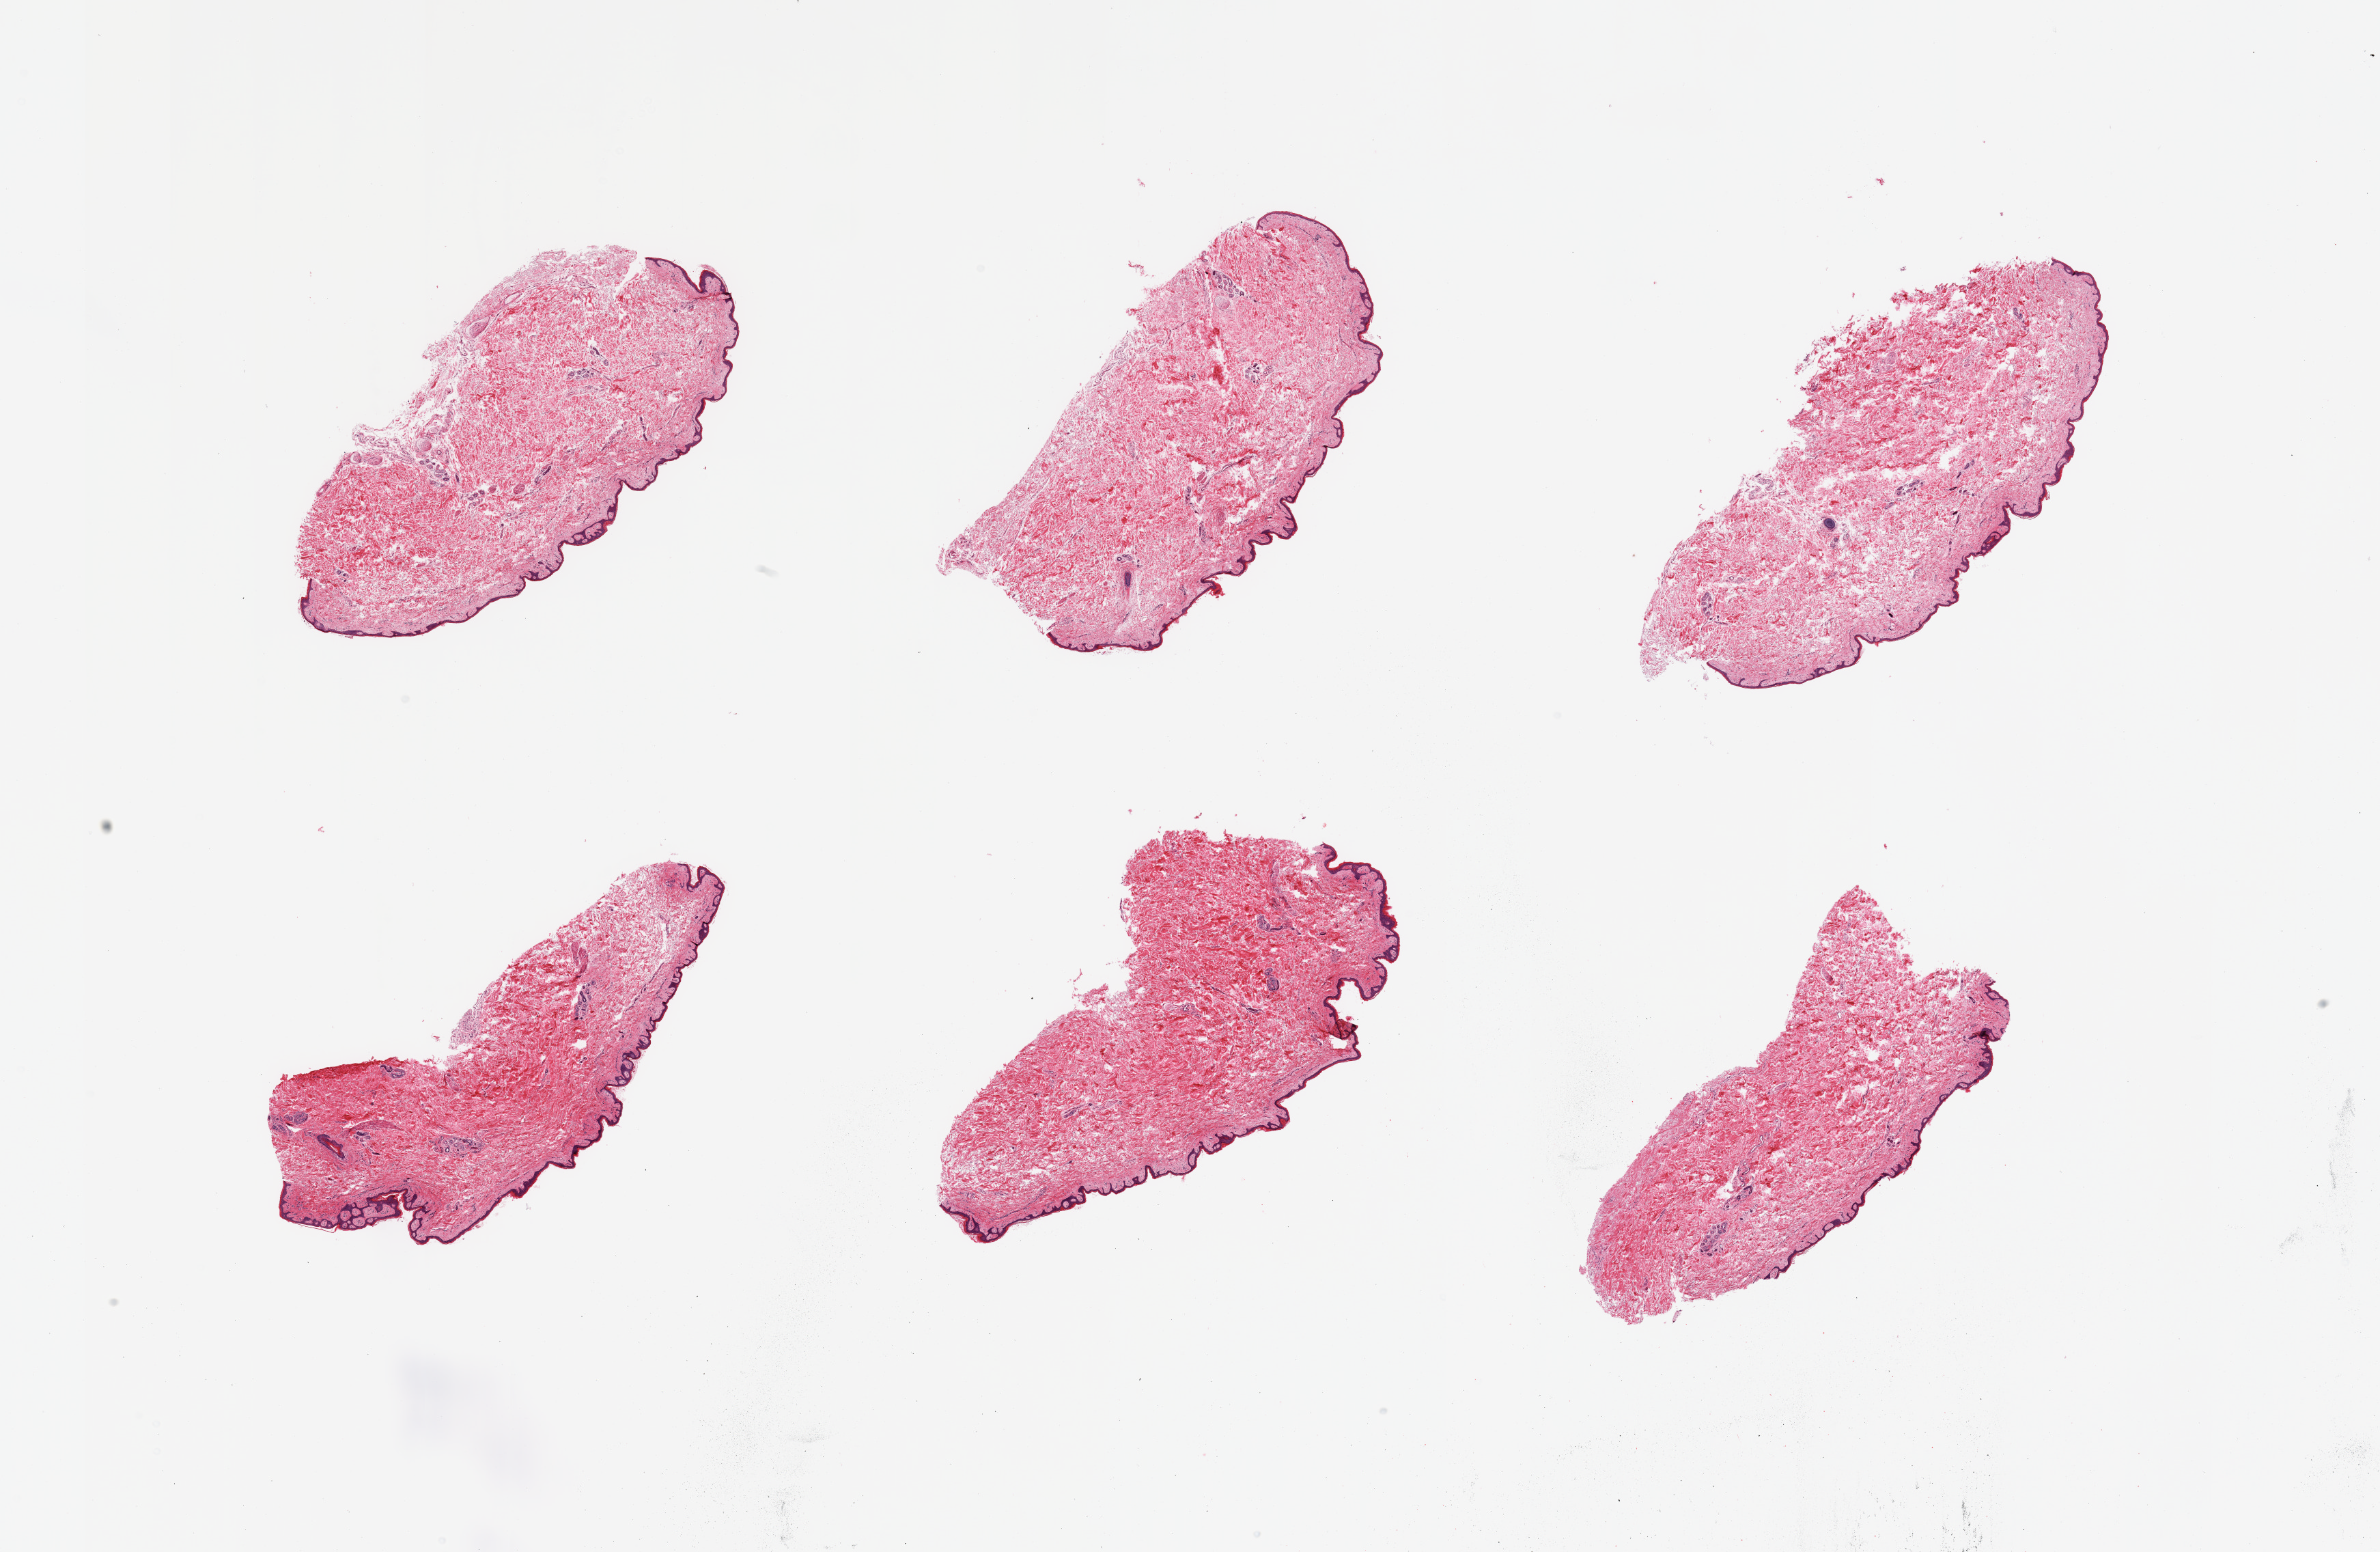
Haematoxylin and eosin whole-slide image — whole scanned area (about 27.6 x 18.0 mm) shown as a low-resolution overview, PAXgene-fixed, paraffin-embedded tissue, sampled site (target tissue): skin of suprapubic region, donor tissue sample. Donor sex: male.
* pathologist's review note for this sample: 6 pieces; well trimmed